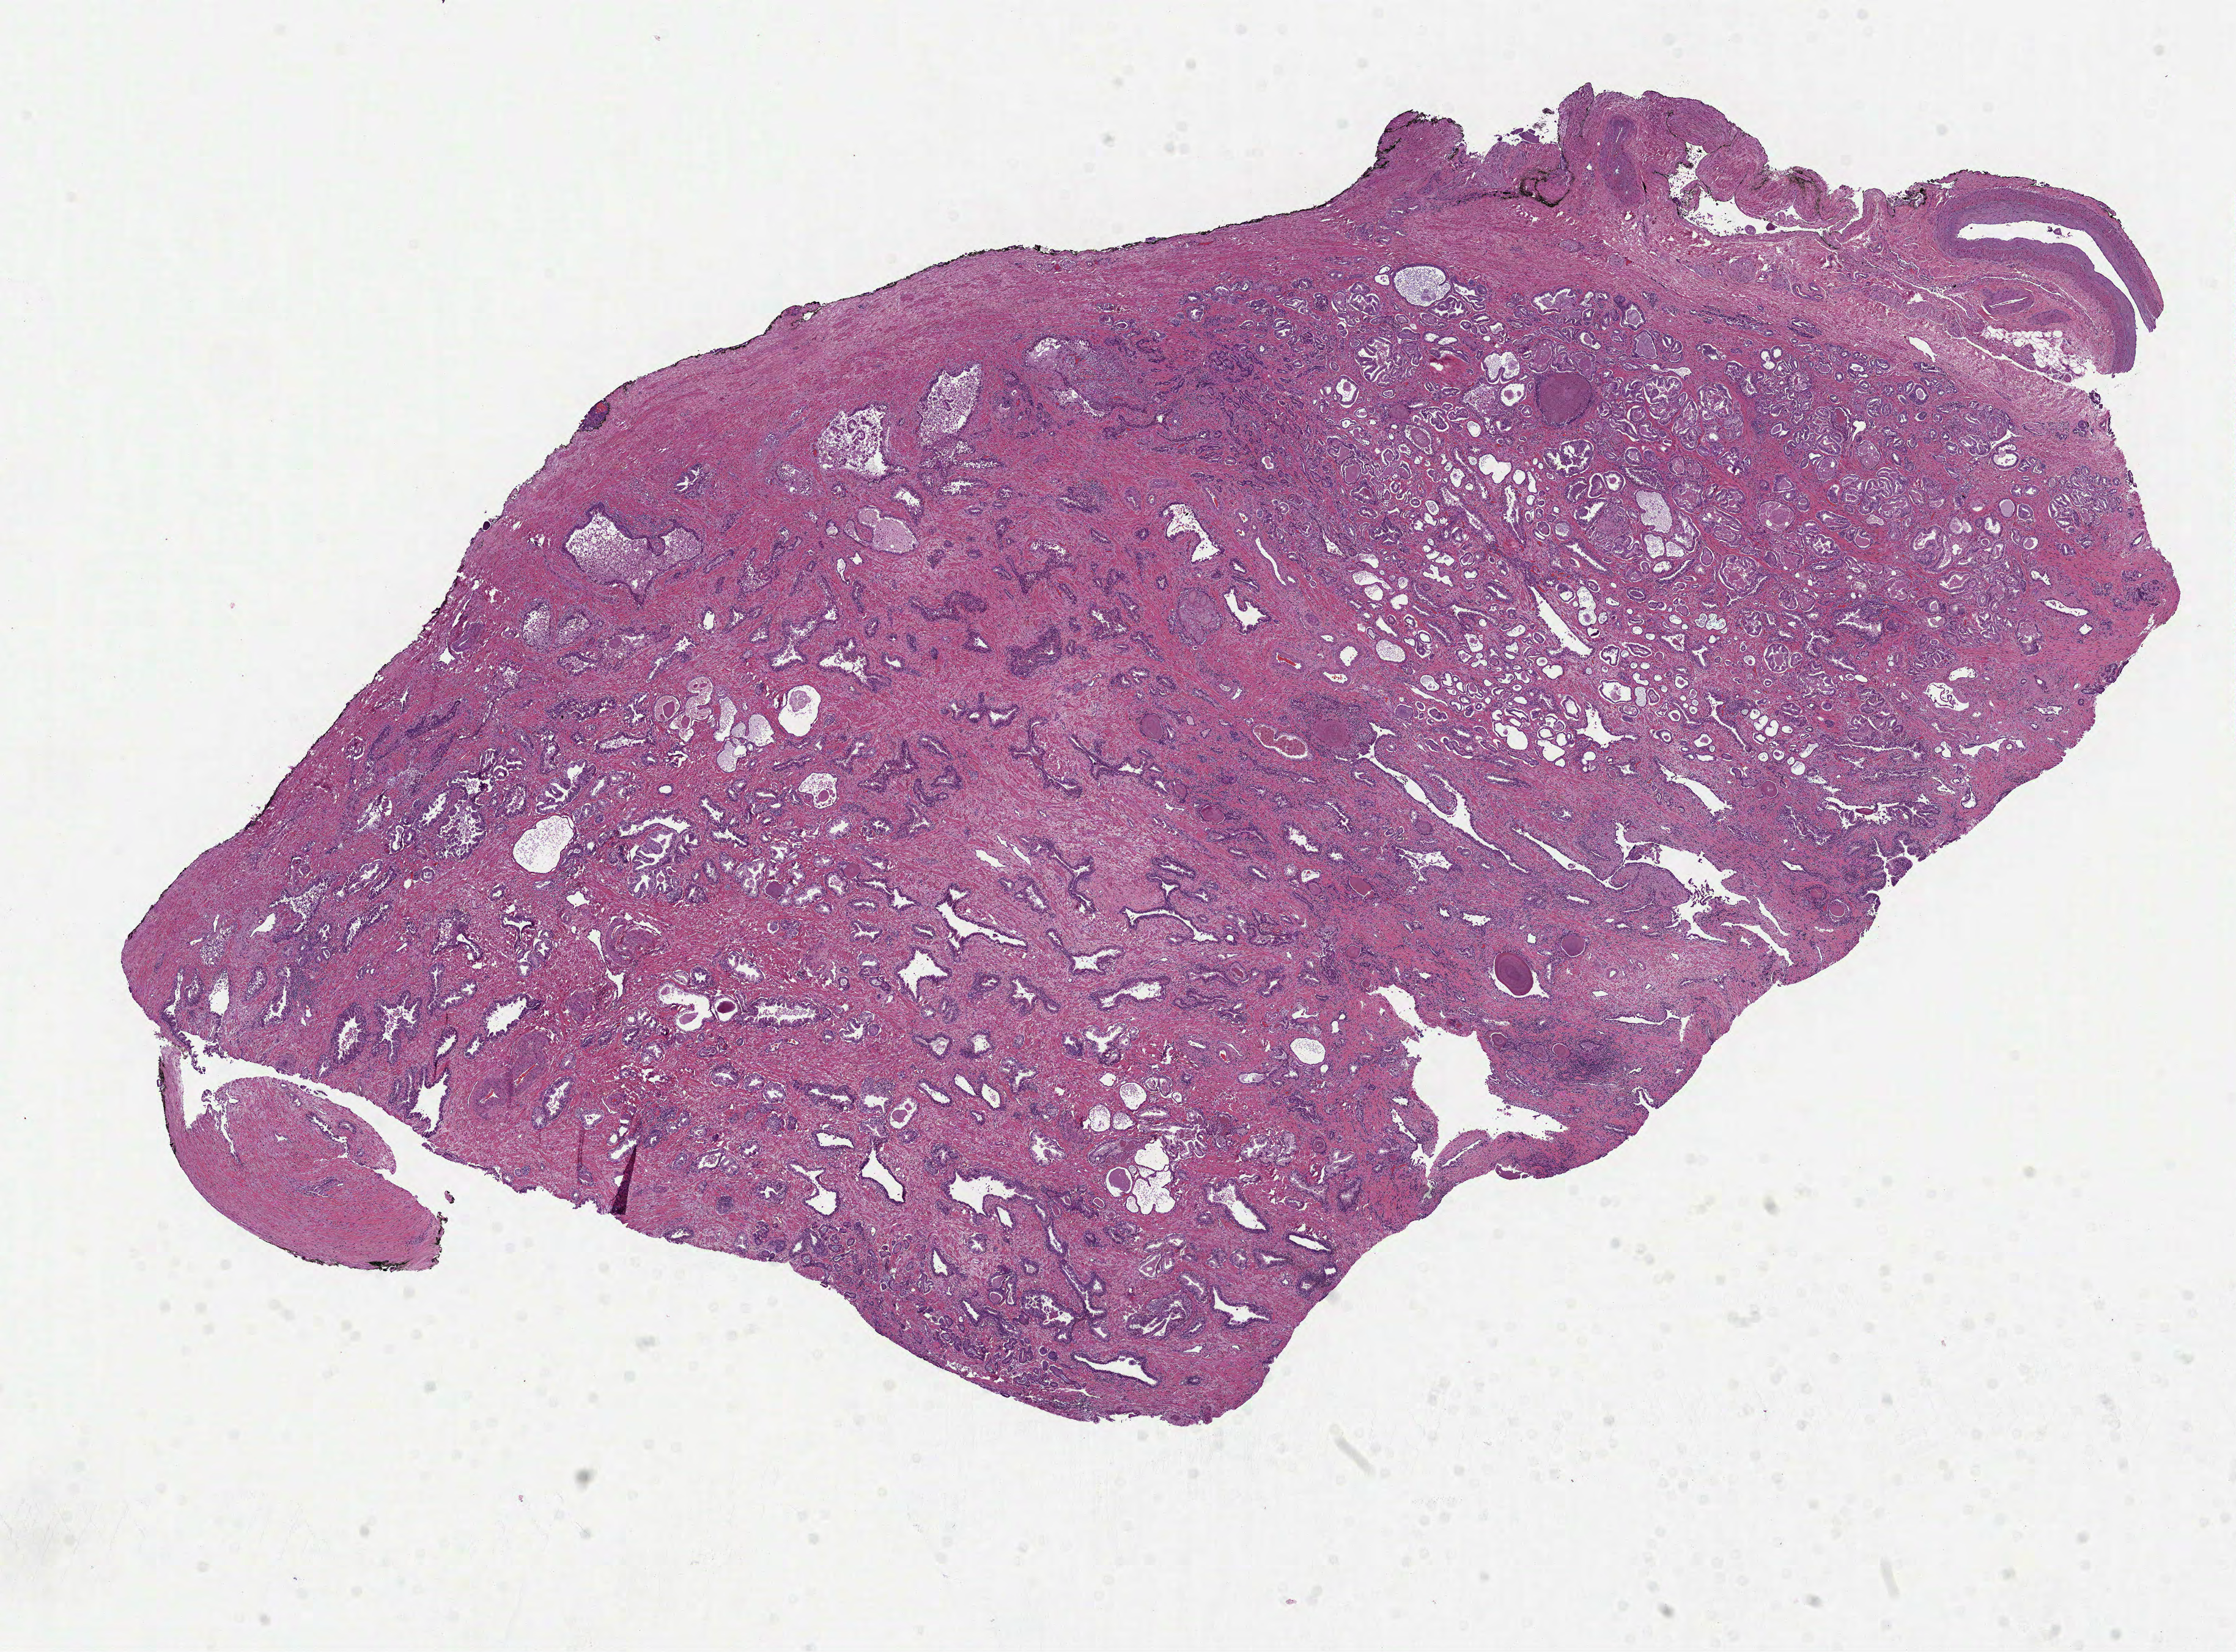
H&E-stained whole-slide image, low-resolution overview of the scanned area, about 14.7 x 10.9 mm (acquisition: 40x scan), FFPE section, prostate, primary tumour sample. Male patient; age at initial diagnosis 66 years. Gleason score: 7 (3+4).
- lymph nodes positive (case pathology): 0 of 6 examined
- histologic diagnosis: Acinar cell carcinoma (prostate gland)